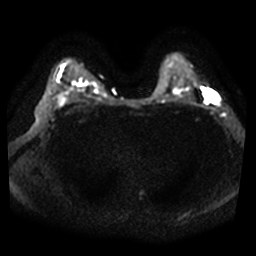
Breast MRI, one axial slice. Slice 29 of 38 in the series (ordered by position). Diffusion-weighted series; image 2 of 4 stored at this slice position (different b-values; order by instance number). 3 T. 256 × 256 image matrix, field of view 360 × 360 mm. Female patient.
Structures marked on this image (manually delineated by an expert):
- tumour on diffusion-weighted imaging: bounding box [x1, y1, x2, y2] px = [204, 89, 219, 104]